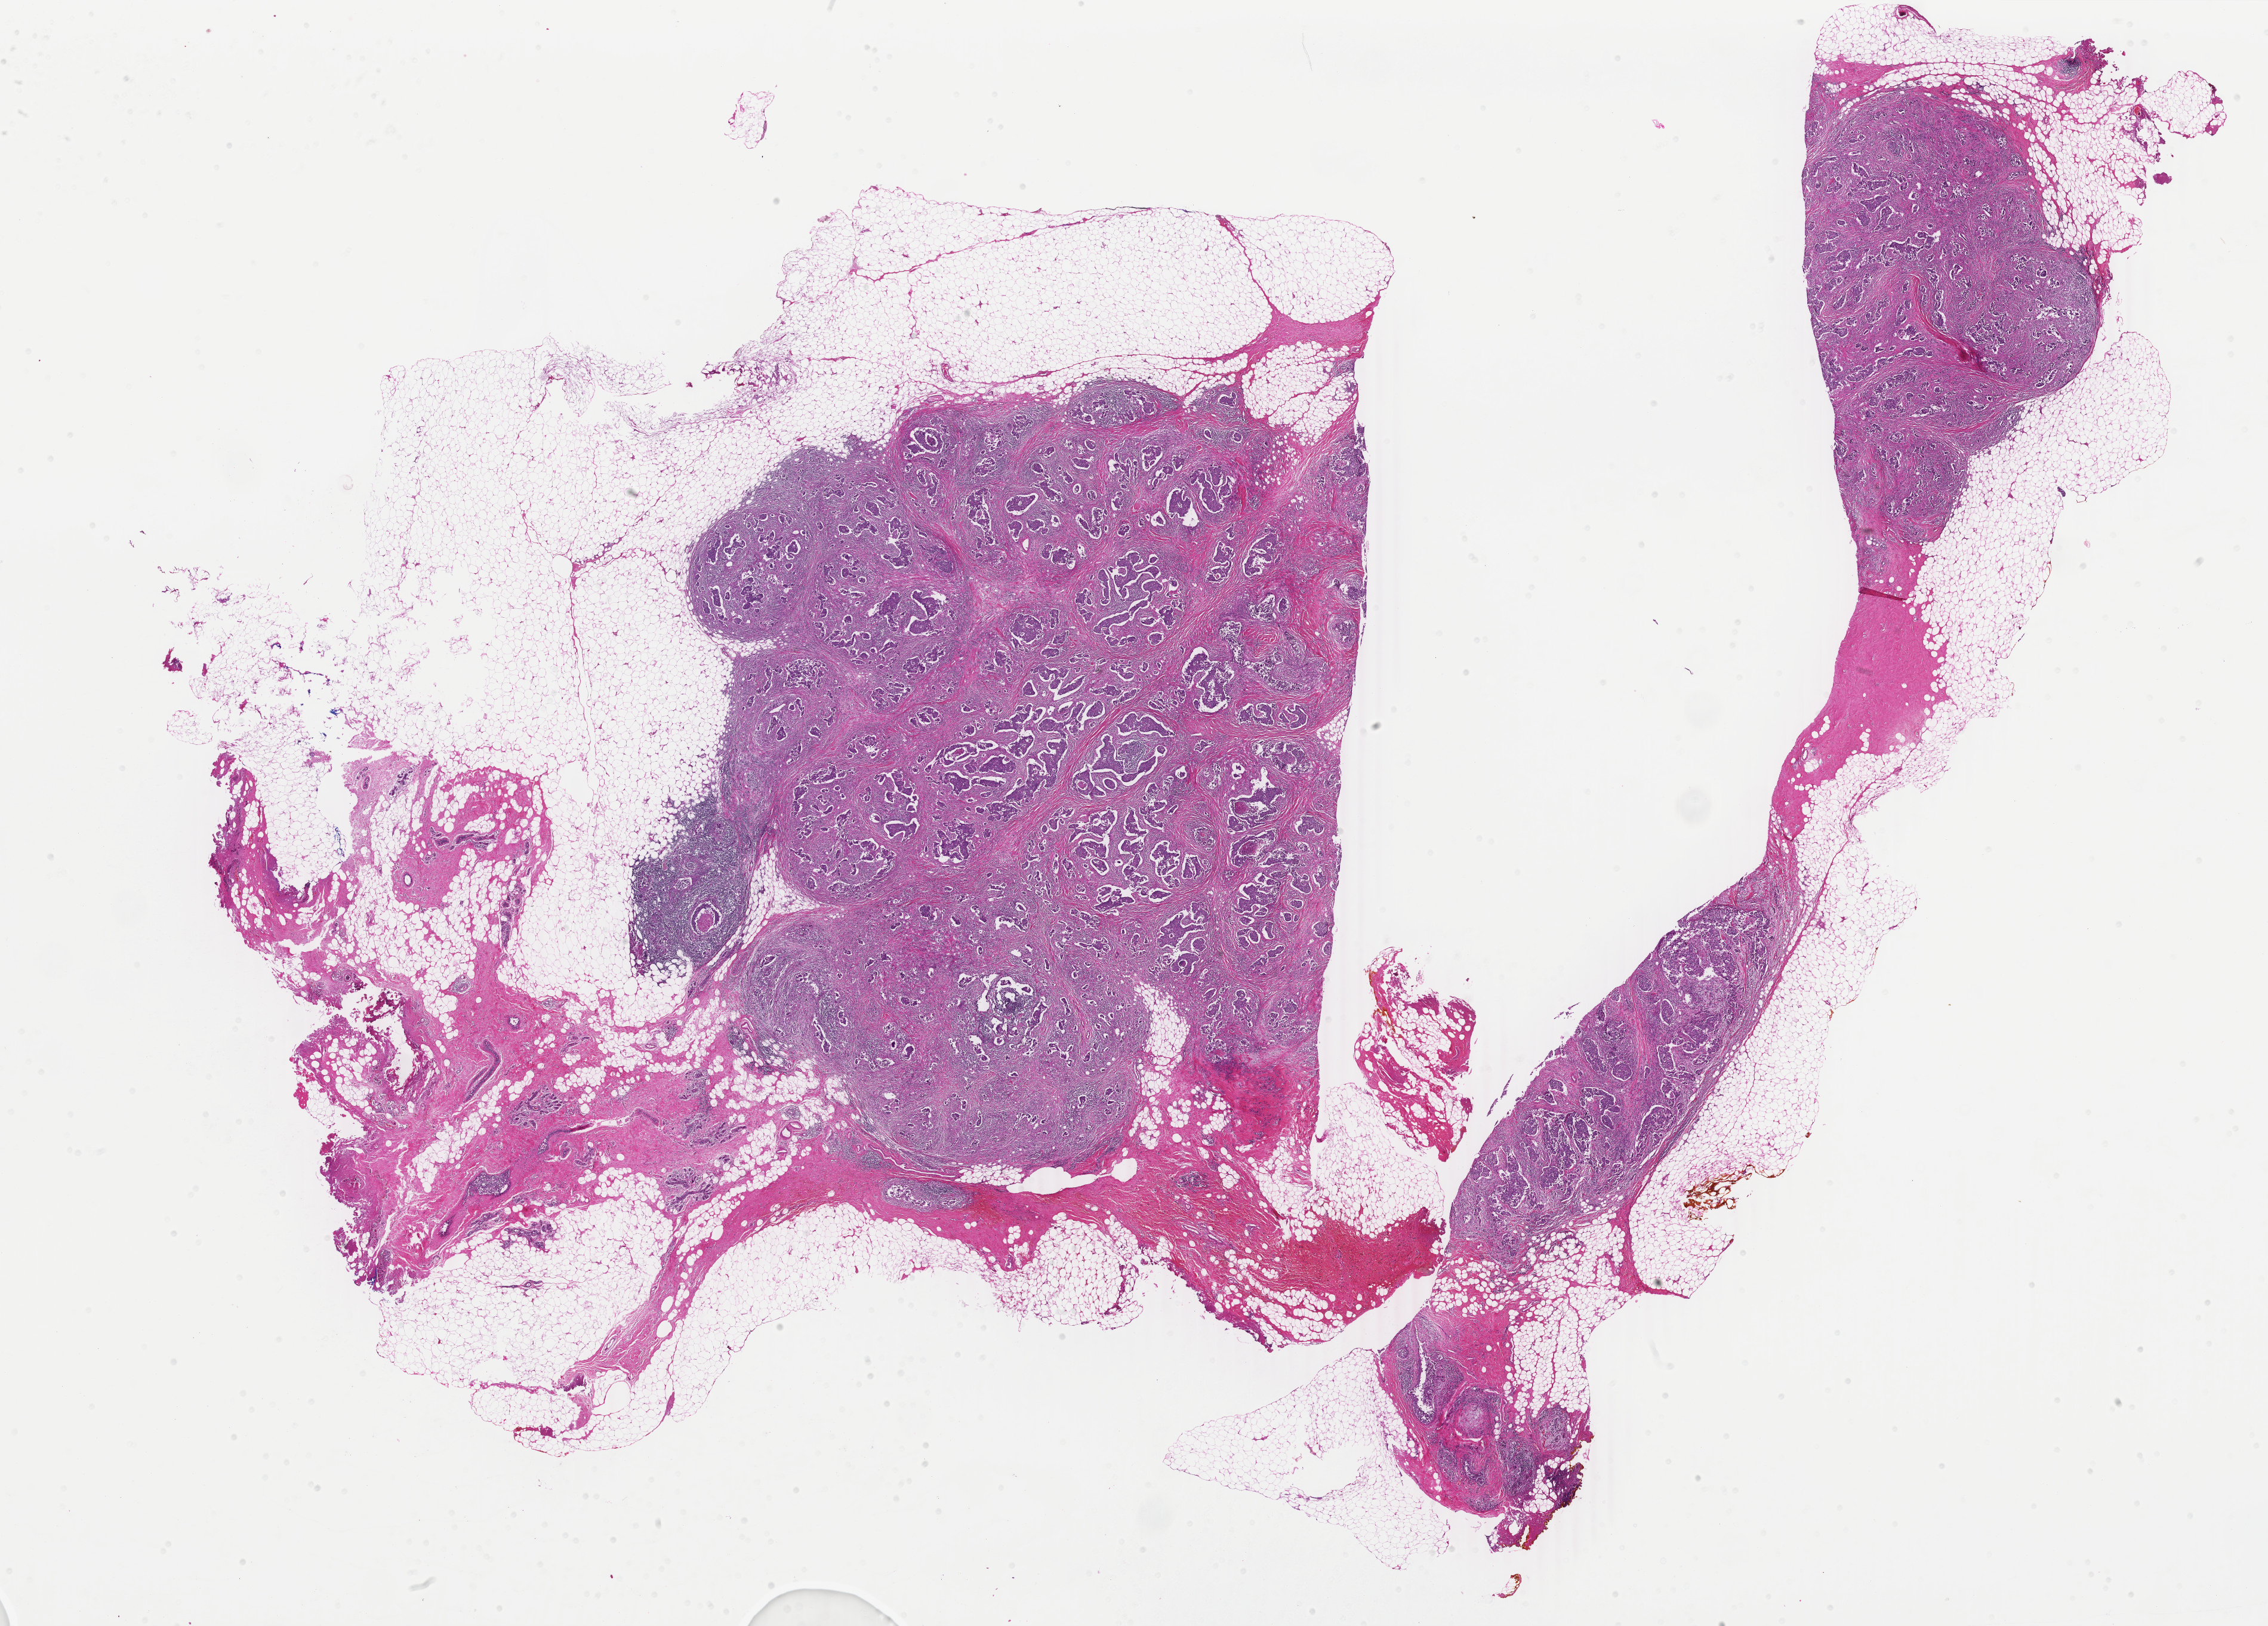
Whole-slide histology image, H&E — shown as a low-resolution overview of the whole scanned area (about 30.2 x 21.7 mm, acquisition: 40x scan), formalin-fixed paraffin-embedded (FFPE) diagnostic section, sample: primary tumour, breast. Female, age 64 years at initial diagnosis.
Lymph nodes positive (case pathology): 0 of 2 examined. Diagnosis: Infiltrating duct carcinoma, NOS. AJCC pathologic stage: IIA (6th edition).